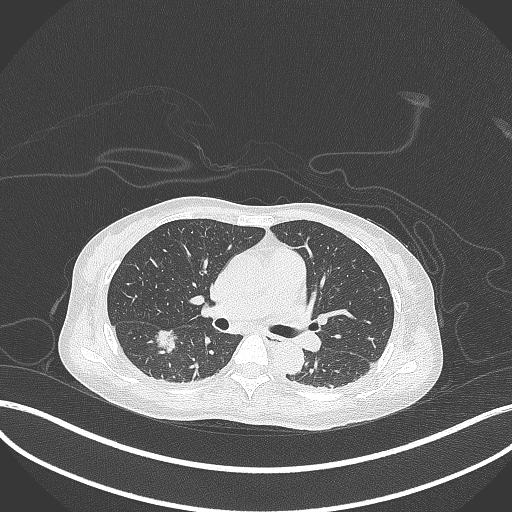
Chest CT, one axial slice. Position 178 of 261 along the scan axis. 120 kVp. Lung window (W 1500 / L -600 HU). 1 mm slice thickness. 512 × 512 image matrix, field of view 400 × 400 mm. Female patient, age 44 years. From the clinical record (not read from this slice): clinical TNM (as recorded): T1c N0 M0.
Outlined on this slice (bounding box drawn by a radiologist):
- lung tumour (recorded histology: adenocarcinoma): bounding box <157,331,181,357> (left, top, right, bottom; pixels)